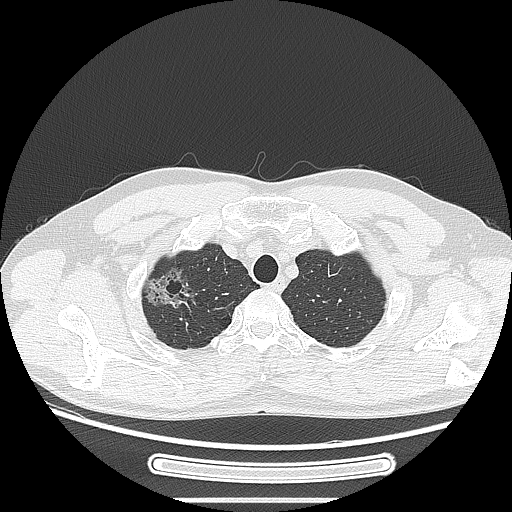
Chest CT, one axial slice; position 229 of 269 along the scan axis; reconstruction kernel LUNG; 120 kVp; lung window (W 1500 / L -600 HU); 1.25 mm slice thickness; 512 × 512 image matrix, field of view 382 × 382 mm. Patient: male, 53 years. From the clinical record (not read from this slice): clinical TNM (as recorded): T1c N0 M0; histopathological grade: G2.
Annotated regions visible in this slice (rectangle marked by the reading radiologist):
- lung tumour (recorded histology: adenocarcinoma): bounding box <126,261,207,317> (left, top, right, bottom; pixels)